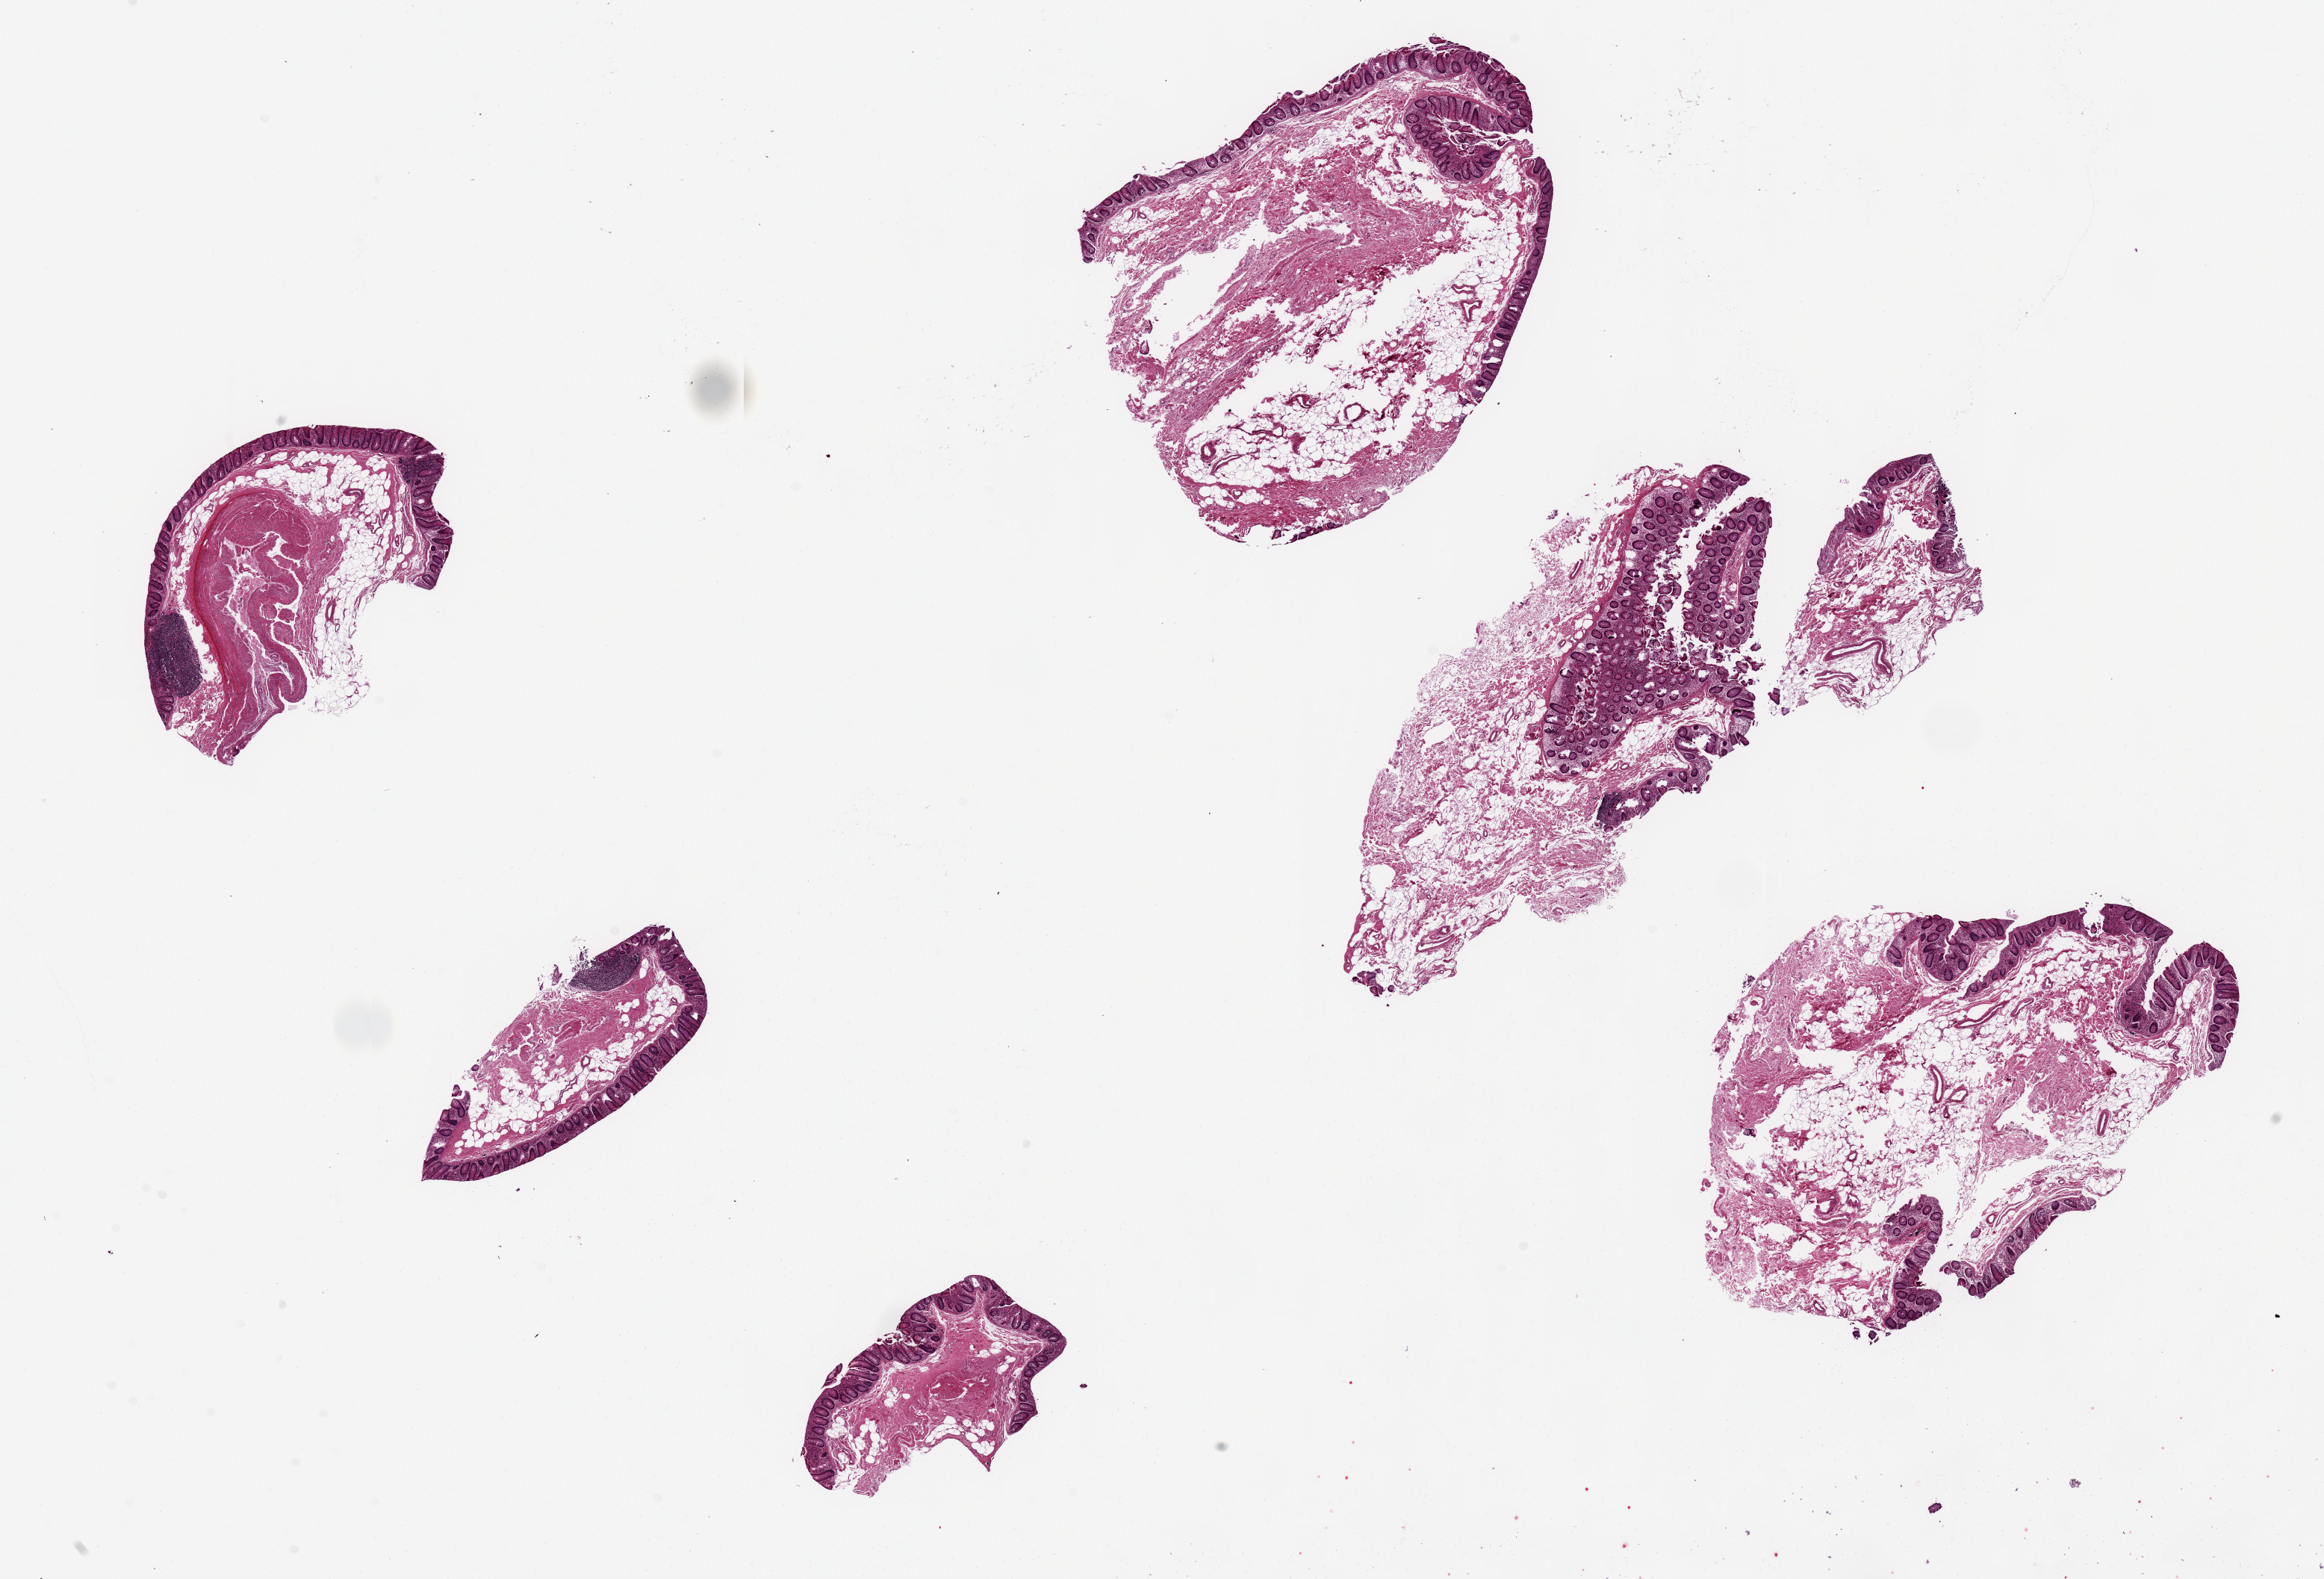
Digitized hematoxylin and eosin (H&E)-stained section — whole scanned area (about 24.6 x 16.7 mm, from a 20x scan) shown as a low-resolution overview, PAXgene-fixed paraffin-embedded (PFPE) section, section of transverse colon (target tissue), donor tissue sample. Male donor.
Pathologist's review note for this sample: 6 ~4.5x3.5mm pieces; mucosa variably preserved, 5-10% of thickness.